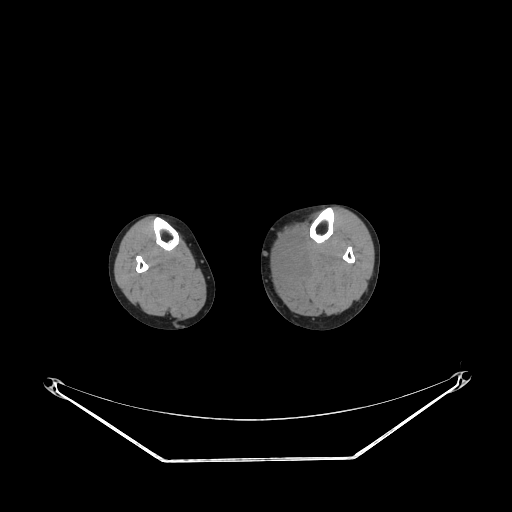
CT of an extremity soft-tissue mass (from a PET/CT study), one axial slice; position 131 of 223 along the scan axis; reconstruction kernel STANDARD; soft-tissue window (W 400 / L 40 HU); 3.75 mm slice thickness; 512 × 512 image matrix, field of view 500 × 500 mm. Female patient. From the clinical record (not read from this slice): histological type: extraskeletal high grade osteogenic sarcoma; grade: high; site of the primary tumour: left calf.
Structures marked on this image (expert contour drawn on MRI and transferred to this co-registered scan by the dataset authors):
- gross tumour volume (mass): bounding box <279,246,305,275> (left, top, right, bottom; pixels)